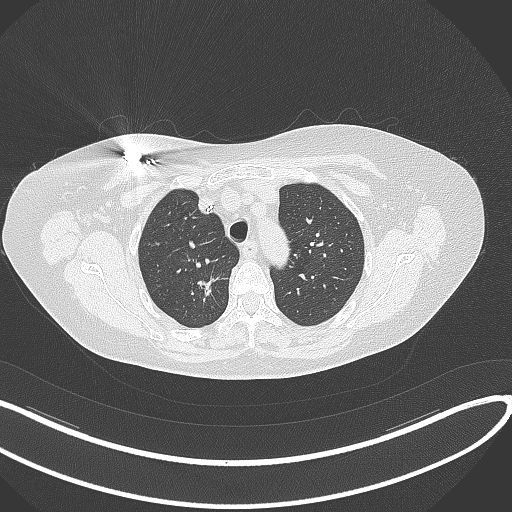
Chest CT, one axial slice; reconstruction kernel B70f; 120 kVp; lung window (W 1500 / L -600 HU); 1 mm slice thickness; 512 × 512 image matrix. Female patient, age 72 years. Case-level facts recorded for this patient, not image findings: clinical TNM (as recorded): T1c N0 M0.
Structures marked on this image (rectangle marked by the reading radiologist):
- lung tumour (recorded histology: adenocarcinoma): bounding box [x1, y1, x2, y2] px = [194, 269, 229, 309]